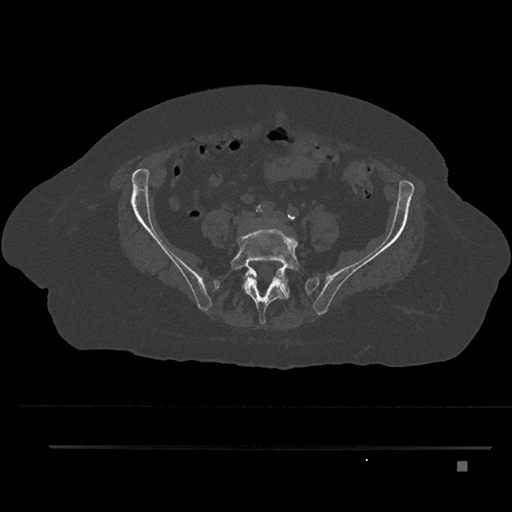
CT including the spine, one axial slice; position 39 of 797 along the scan axis; 120 kVp; bone window (W 1800 / L 400 HU); 0.5 mm slice thickness; 512 × 512 image matrix, field of view 437 × 437 mm. Patient: female, 76 years. Case-level facts recorded for this patient, not image findings: primary cancer: lung.
Structures marked on this image (semi-automatically segmented with operator editing):
- L4 vertebra: bounding box [x1, y1, x2, y2] px = [249, 272, 285, 283]
- L5 vertebra: [230, 222, 300, 325]